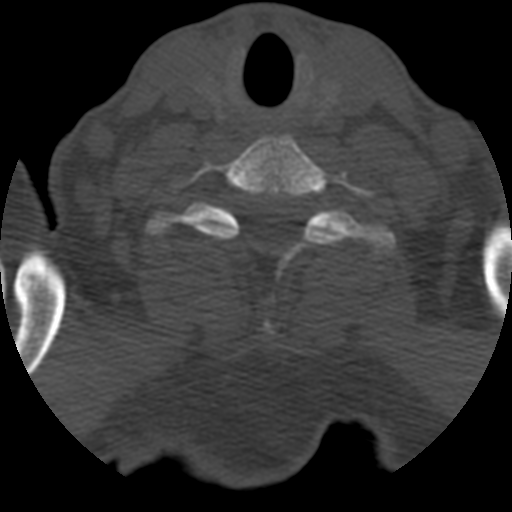
CT including the spine, one axial slice; slice 527 of 708 in the series (ordered by position); one of 3 acquisitions stored at this slice position; bone window (W 1800 / L 400 HU); 1.25 mm slice thickness; 512 × 512 image matrix, field of view 160 × 160 mm. Patient age 55 years. Case-level facts recorded for this patient, not image findings: primary cancer: colon; vertebrae with lytic lesions (as recorded): T12, L1, L5.
Annotated regions visible in this slice (semi-automatic segmentation, software-assisted and operator-edited):
- T1 vertebra: box from (x=144, y=201) to (x=396, y=259) px